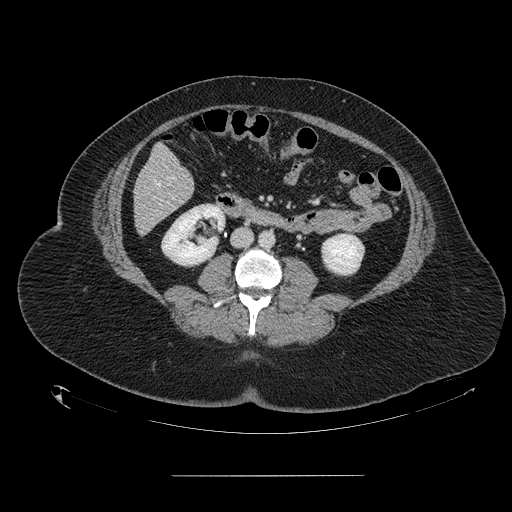
Contrast-enhanced abdominal CT, one axial slice. 120 kVp. Intravenous contrast given. Soft-tissue window (W 400 / L 40 HU). 512 × 512 image matrix, field of view 495 × 495 mm. Female patient, age 52 years. From the clinical record (not read from this slice): diagnosis: colorectal cancer liver metastases, imaged before liver resection; multiple liver metastases: yes; largest metastasis: 3.5 cm; disease in both lobes: no.
Outlined on this slice (manually delineated by an expert):
- hepatic veins: bounding box [x1, y1, x2, y2] px = [154, 181, 160, 186]
- liver: [134, 146, 194, 233]